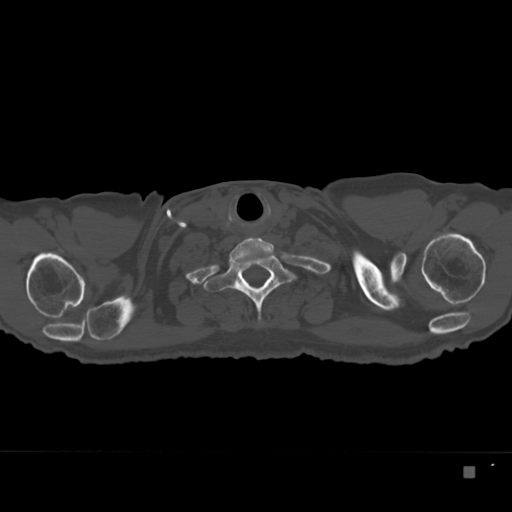
CT including the spine, one axial slice. Position 318 of 332 along the scan axis. Reconstruction kernel Br40s. 120 kVp. Bone window (W 1800 / L 400 HU). 1.5 mm slice thickness. 512 × 512 image matrix, field of view 389 × 389 mm. Male patient, age 72 years. Case-level facts recorded for this patient, not image findings: primary cancer: skeletal.
Outlined on this slice (semi-automatically segmented with operator editing):
- T1 vertebra: bounding box <204,253,295,321> (left, top, right, bottom; pixels)